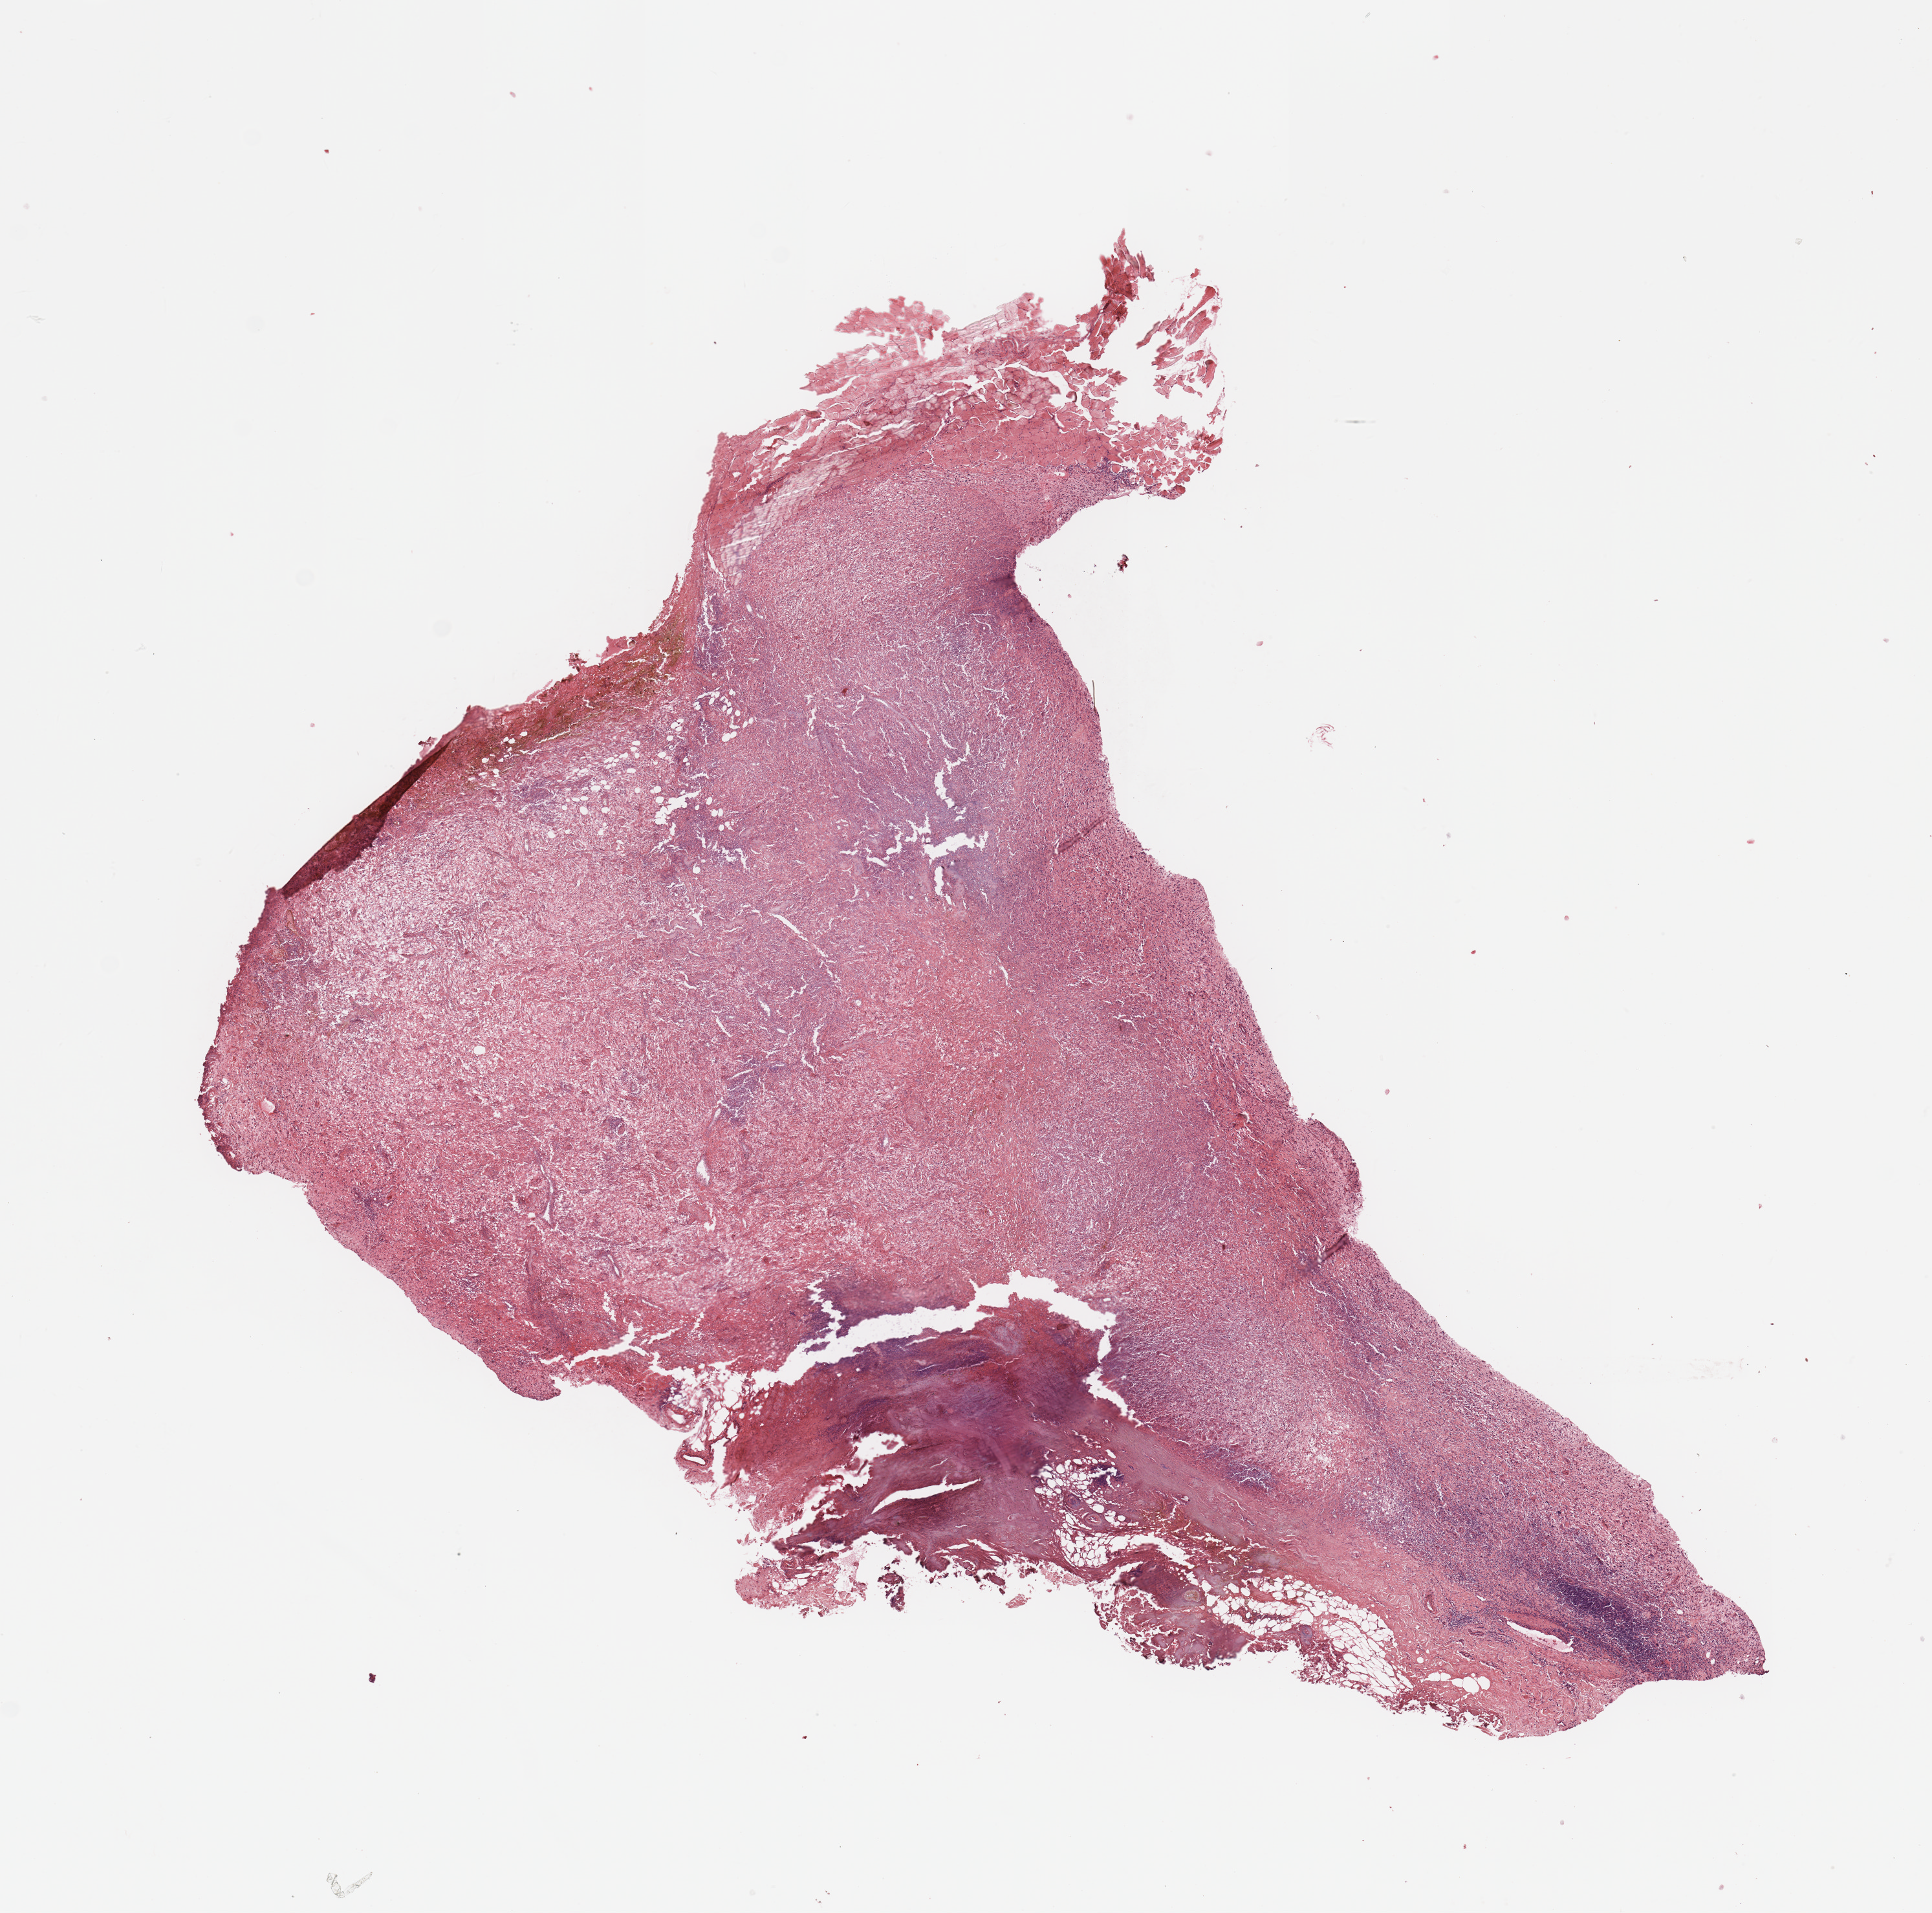
Digitized H&E-stained tissue section (whole slide) — shown as a low-resolution overview of the whole scanned area (about 11.8 x 11.7 mm, from a 20x scan), tumour tissue sample. 53-year-old male patient.
• primary tumour site (as recorded): chest
• patient diagnosis (cohort enrolment): sarcoma (site not recorded at cohort level)